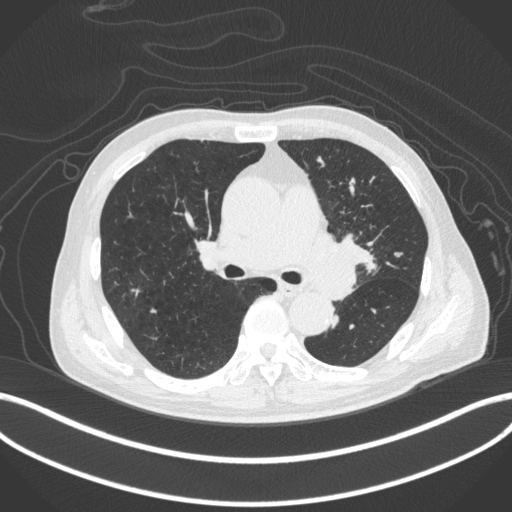
Chest CT, one axial slice; position 259 of 420 along the scan axis; reconstruction kernel B31f; 120 kVp; lung window (W 1500 / L -600 HU); 512 × 512 image matrix, field of view 400 × 400 mm. Male patient, age 77 years. Case-level facts recorded for this patient, not image findings: clinical TNM (as recorded): T3 N1 M0.
Structures marked on this image (rectangle marked by the reading radiologist):
- lung tumour (recorded histology: adenocarcinoma): bounding box (x1, y1, x2, y2) in pixels: (298, 228, 371, 304)